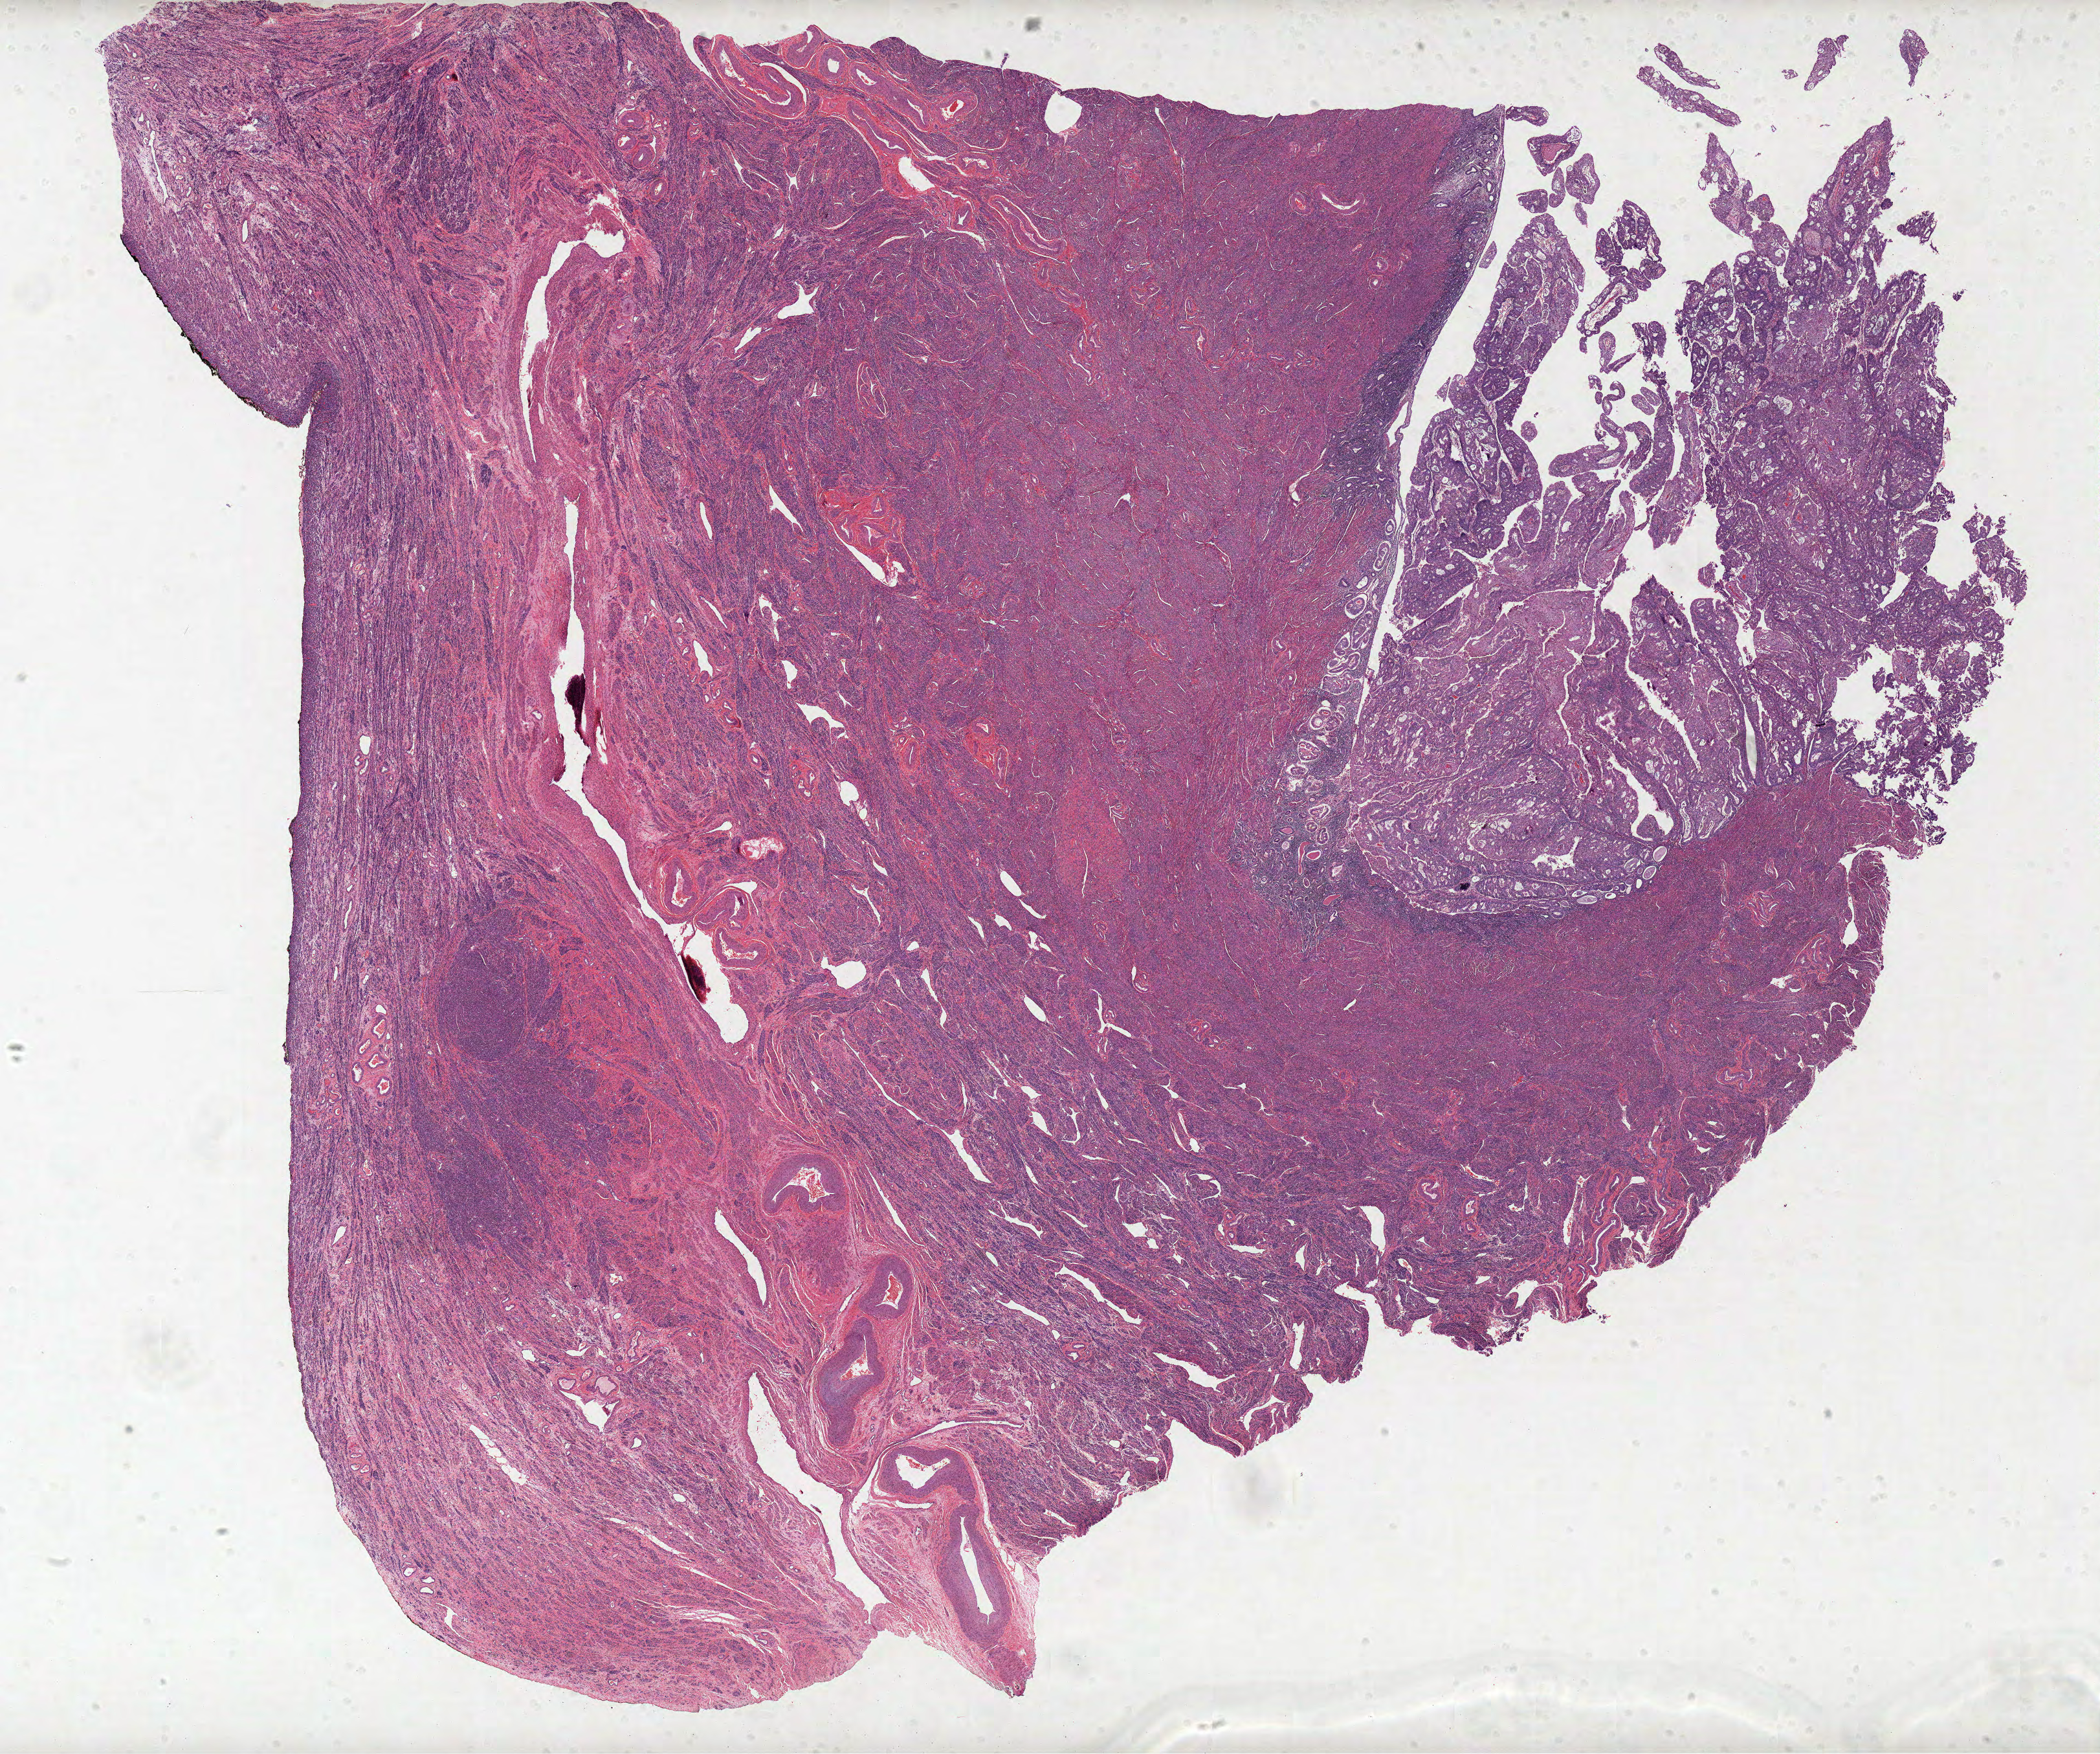
Hematoxylin and eosin (H&E) stained whole-slide image, shown as a low-resolution overview of the whole scanned area (about 25.9 x 21.6 mm), formalin-fixed paraffin-embedded (FFPE) diagnostic section, primary tumour sample from the uterus. Female patient; age at initial diagnosis 59 years. Histologic grade: G2 (moderately differentiated).
FIGO stage: IA. Histologic diagnosis: Endometrioid adenocarcinoma, NOS (endometrium). Lymph nodes positive (case pathology): 0 of 33 examined.